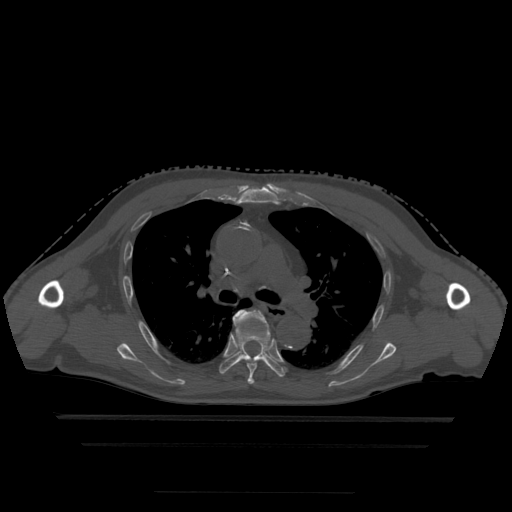
CT including the spine, one axial slice; position 326 of 522 along the scan axis; bone window (W 1800 / L 400 HU); 1.25 mm slice thickness; 512 × 512 image matrix, field of view 436 × 436 mm. Patient age 68 years. Case-level facts recorded for this patient, not image findings: primary cancer: urothelial.
Outlined on this slice (semi-automatic segmentation, software-assisted and operator-edited):
- T5 vertebra: bounding box [x1, y1, x2, y2] px = [233, 310, 265, 385]
- T6 vertebra: [219, 322, 286, 378]